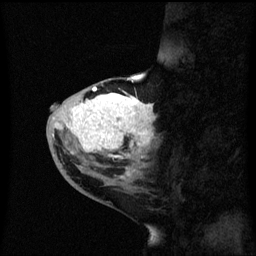
Breast MRI (dynamic contrast-enhanced), one sagittal slice. Slice 23 of 60 in the series (ordered by position). Dynamic contrast-enhanced series, image 2 of 3 at this slice position (ordered by acquisition). 1.5 T. TE 4.2 ms, TR 8.4 ms. 2.3 mm slice thickness. 256 × 256 image matrix, field of view 200 × 200 mm. Female patient, age 46 years. From the clinical record (not read from this slice): setting: breast cancer imaged before/during neoadjuvant chemotherapy; receptor status: HER2-positive.
Annotated regions visible in this slice (semi-automatic segmentation, software-assisted and operator-edited):
- analysis volume of interest (the breast-tissue region the enhancement analysis was run in; not a lesion): box from (x=46, y=86) to (x=159, y=171) px
- tumour enhancement mask (voxels above the 70 % enhancement threshold inside the analysis volume of interest): (x=56, y=86)–(x=155, y=159)